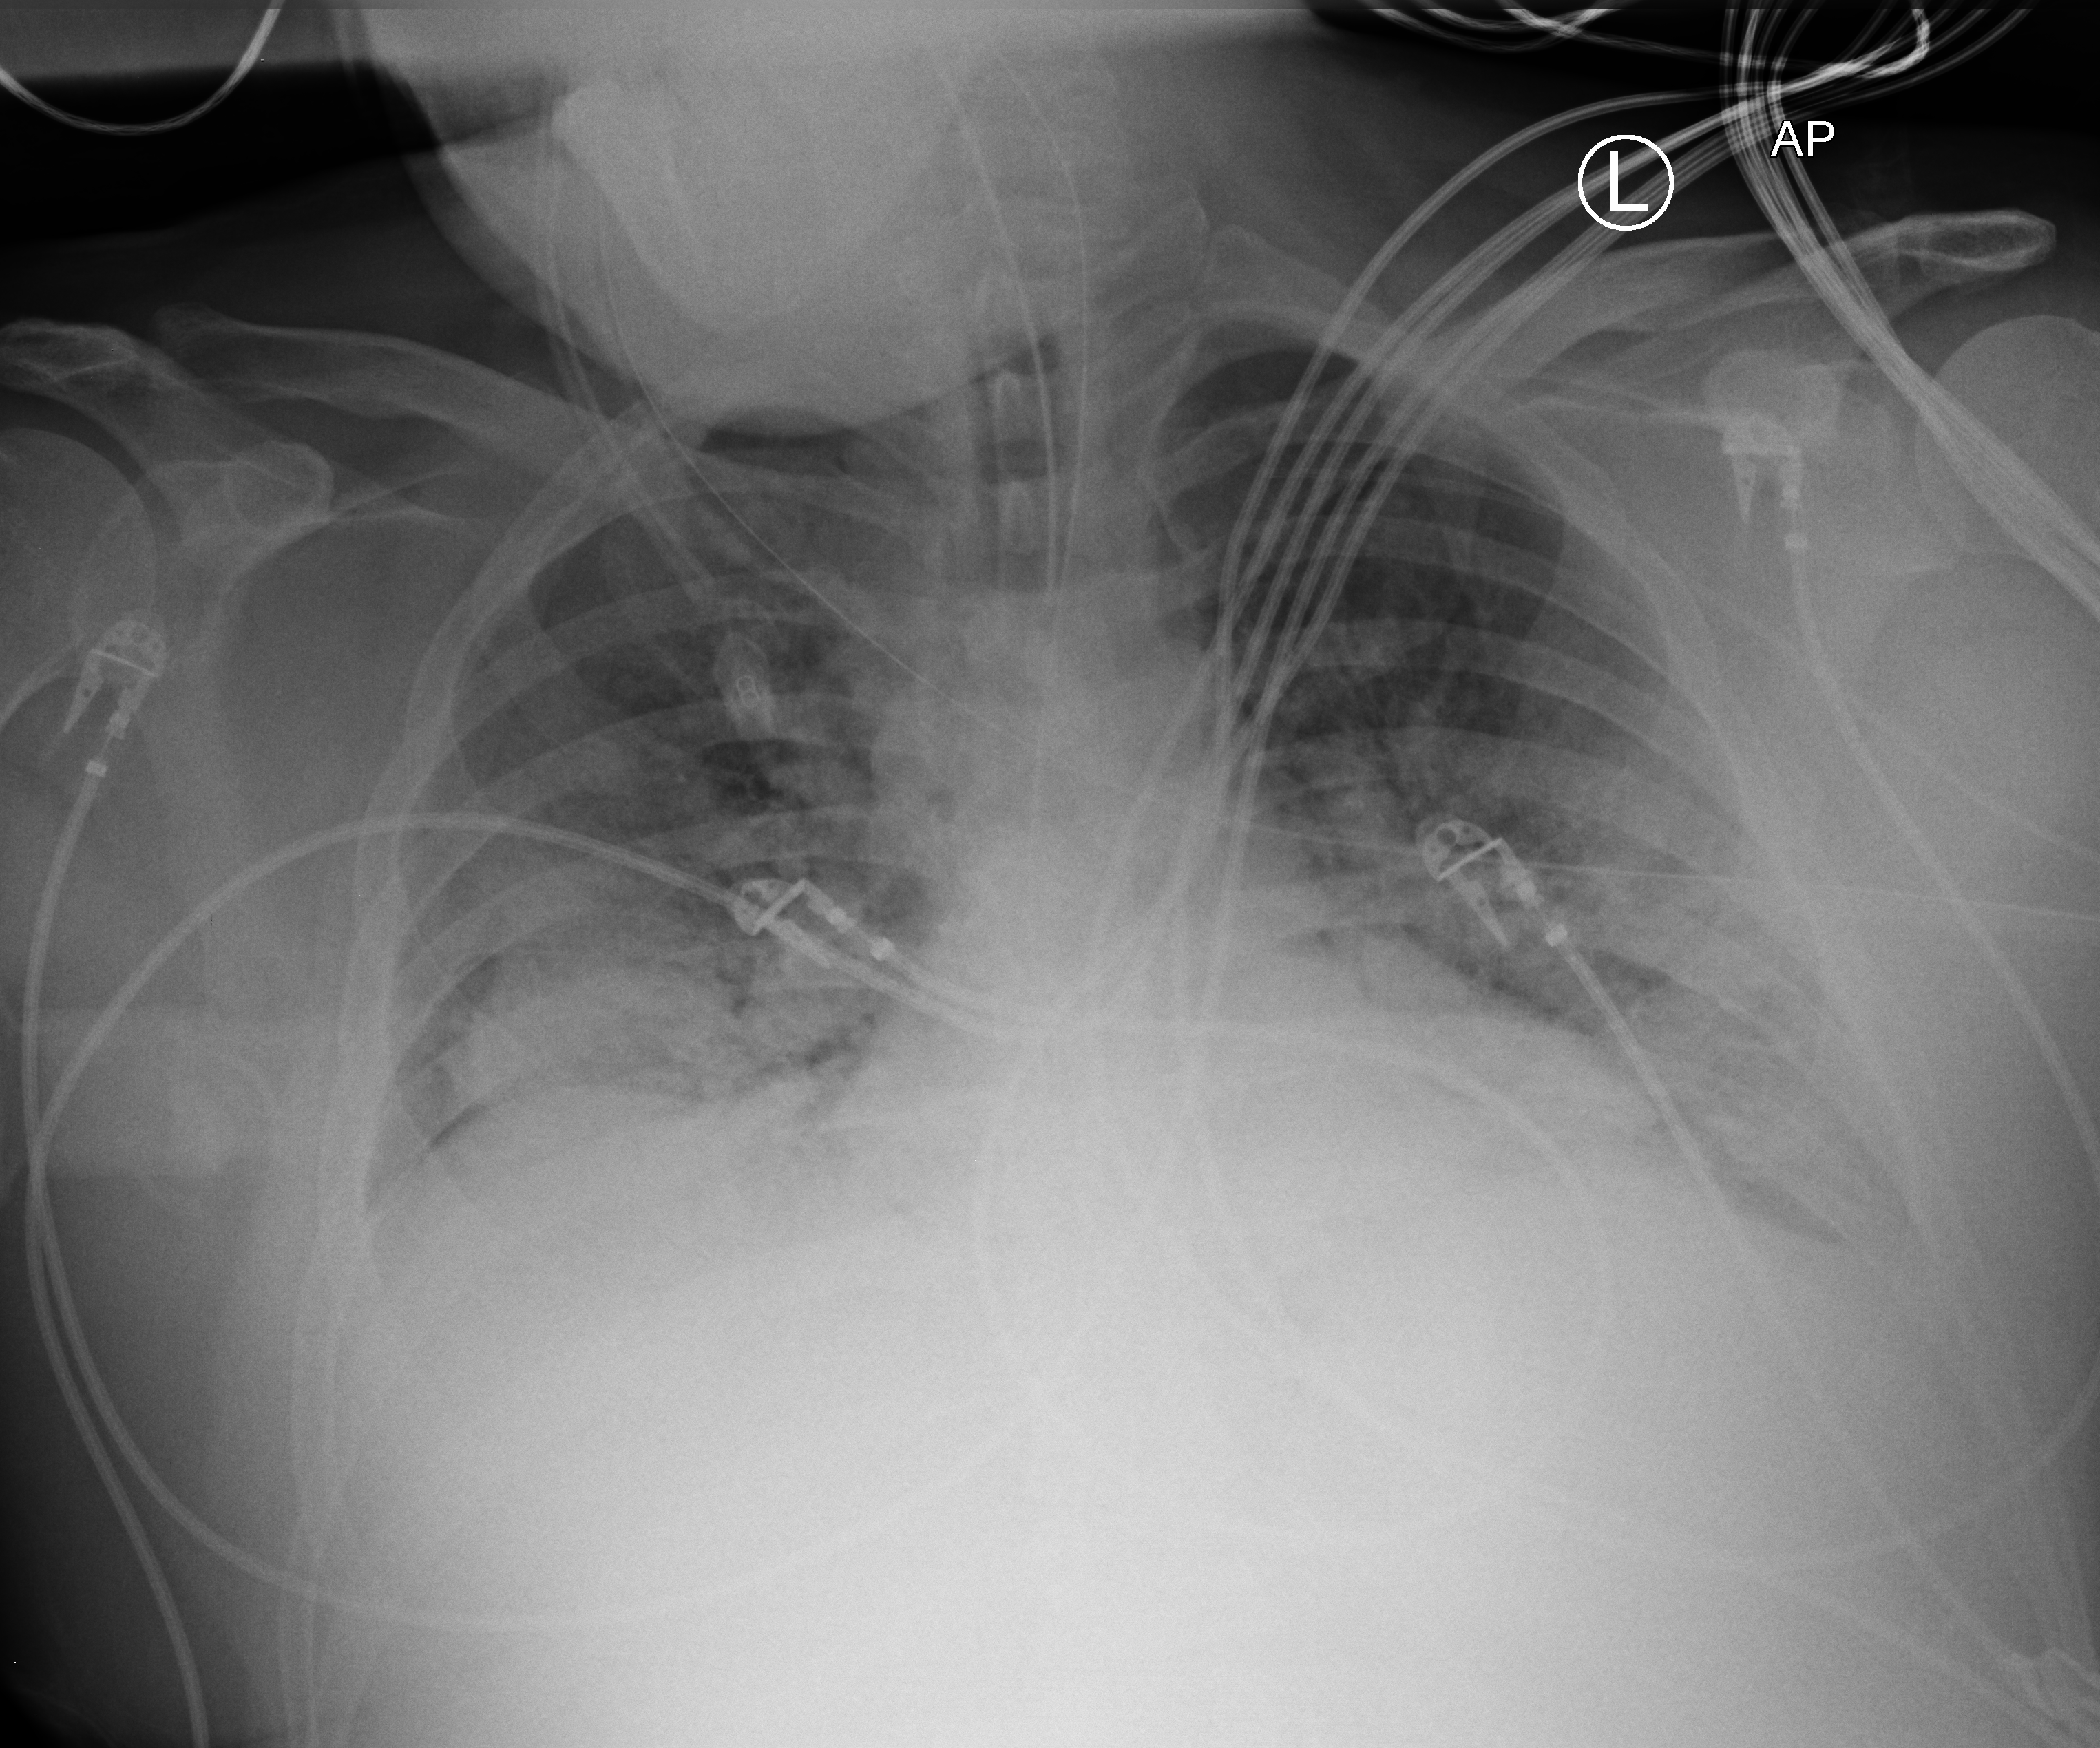
Bedside chest radiograph (computed radiography). Male patient hospitalised with COVID-19, age 18–59 years.
From the hospital-stay record, not from the radiograph (when in the stay this image was taken is not recorded): mechanically ventilated during this hospital stay: yes.